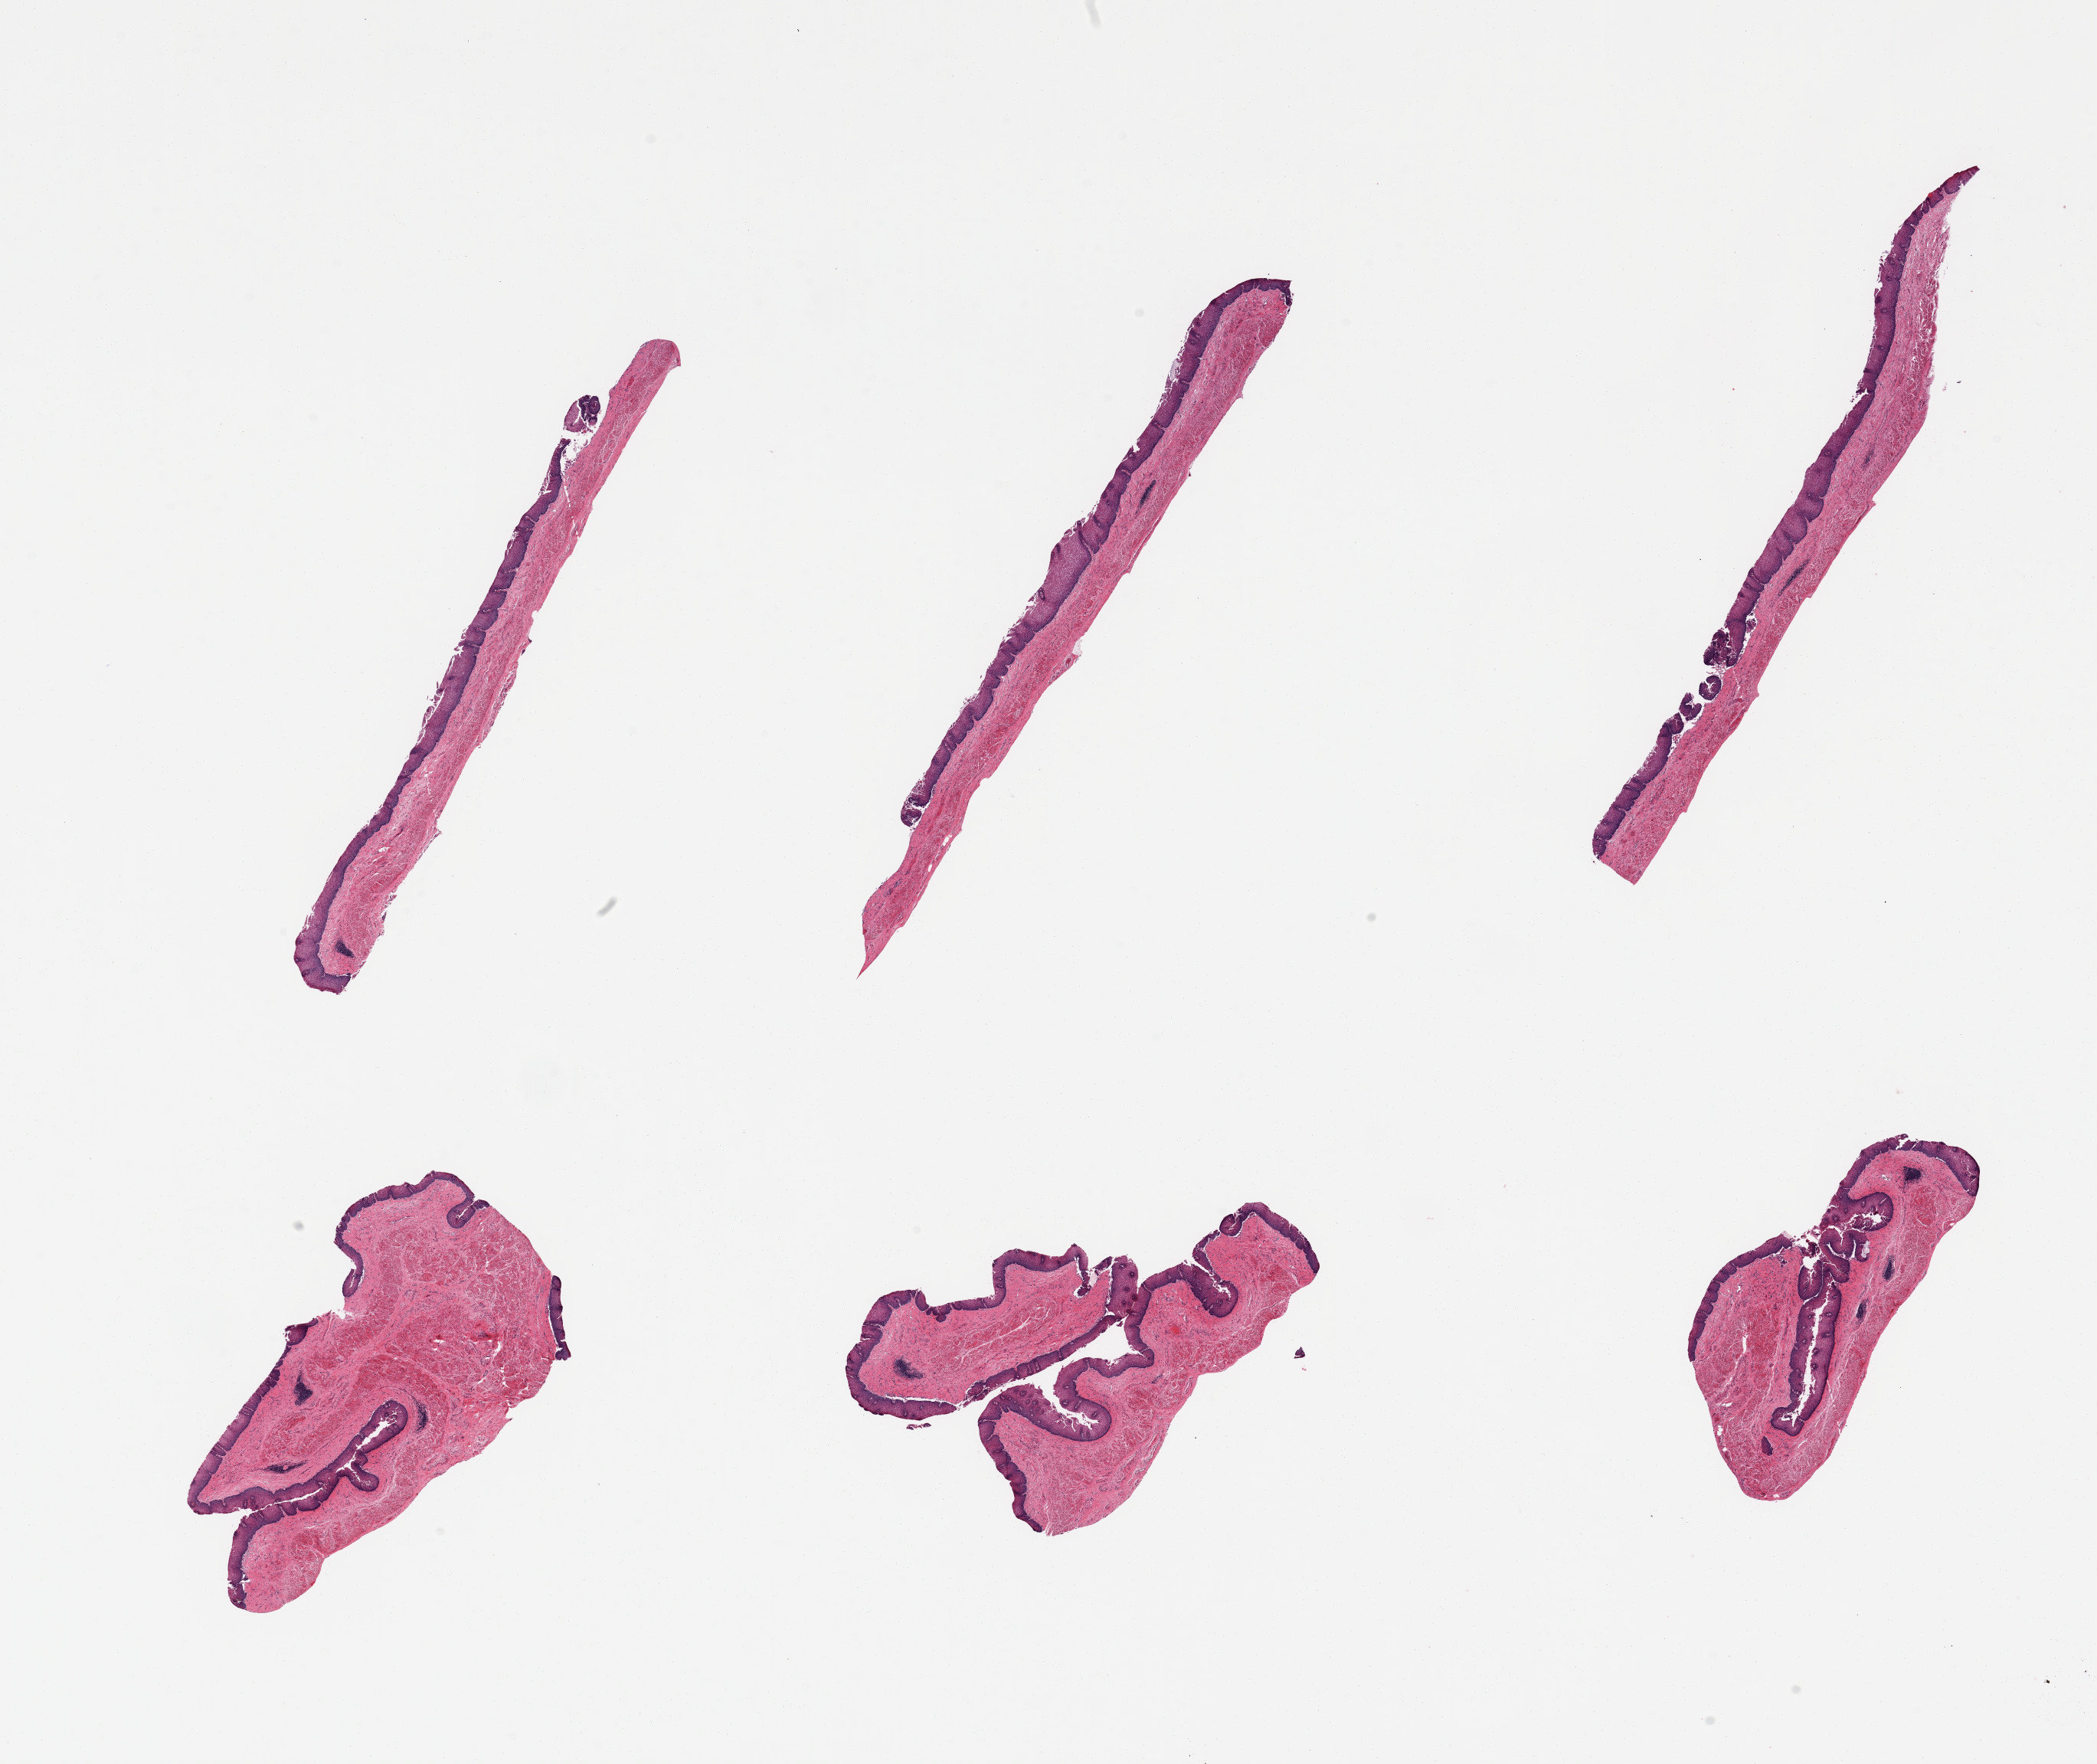
Digitized haematoxylin and eosin-stained section, a low-resolution overview of the entire scanned area, about 21.7 x 18.2 mm; PAXgene-fixed paraffin-embedded (PFPE) section; sampled site (target tissue): esophageal mucous membrane; tissue donor sample. Donor sex: male.
Review note (as recorded): 6 pieces; epithelium moderately fragmented.